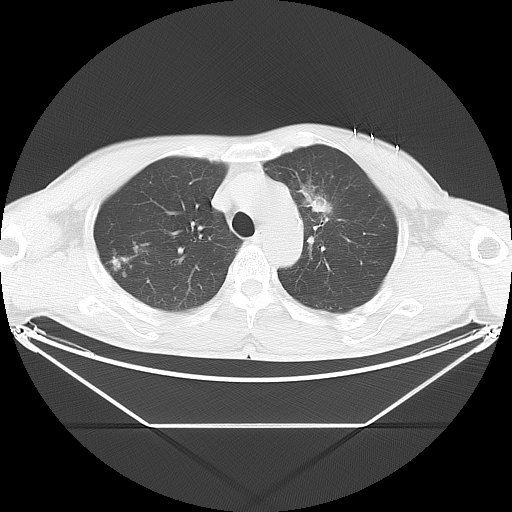
Chest CT, one axial slice. Slice 19 of 28 in the series (ordered by position). 120 kVp. Lung window (W 1500 / L -600 HU). 512 × 512 image matrix, field of view 443 × 443 mm. Male patient, age 60 years. Case-level facts recorded for this patient, not image findings: clinical TNM (as recorded): T2 N1 M0.
Outlined on this slice (rectangle marked by the reading radiologist):
- lung tumour (recorded histology: adenocarcinoma): bounding box <298,184,337,216> (left, top, right, bottom; pixels)